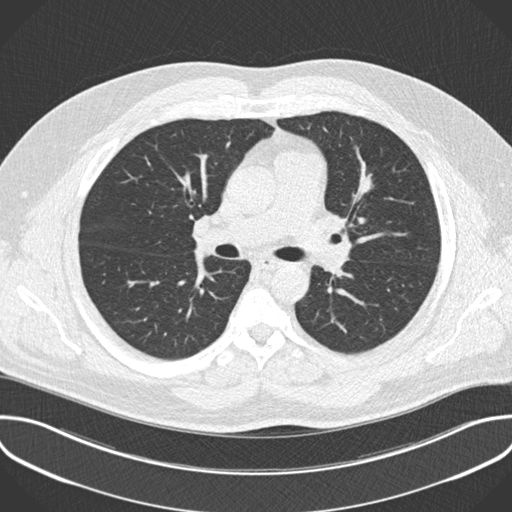
Axial slice from a low-dose chest CT screening exam; baseline annual screen; lung window (W 1500 / L -600 HU); standard (soft-tissue) reconstruction kernel (B30f); slice 72 of 201 in the series; 512 × 512 image matrix. Male participant, aged 55 years at enrolment. Former smoker at enrolment.
Expert-annotated lung lesion, box from (x=347, y=160) to (x=389, y=195) px. Reader record for this screening exam (exam-level; its link to the box is not recorded): non-calcified nodule or mass ≥4 mm, lingula, 13 × 12 mm, spiculated (stellate) margins, soft tissue attenuation.